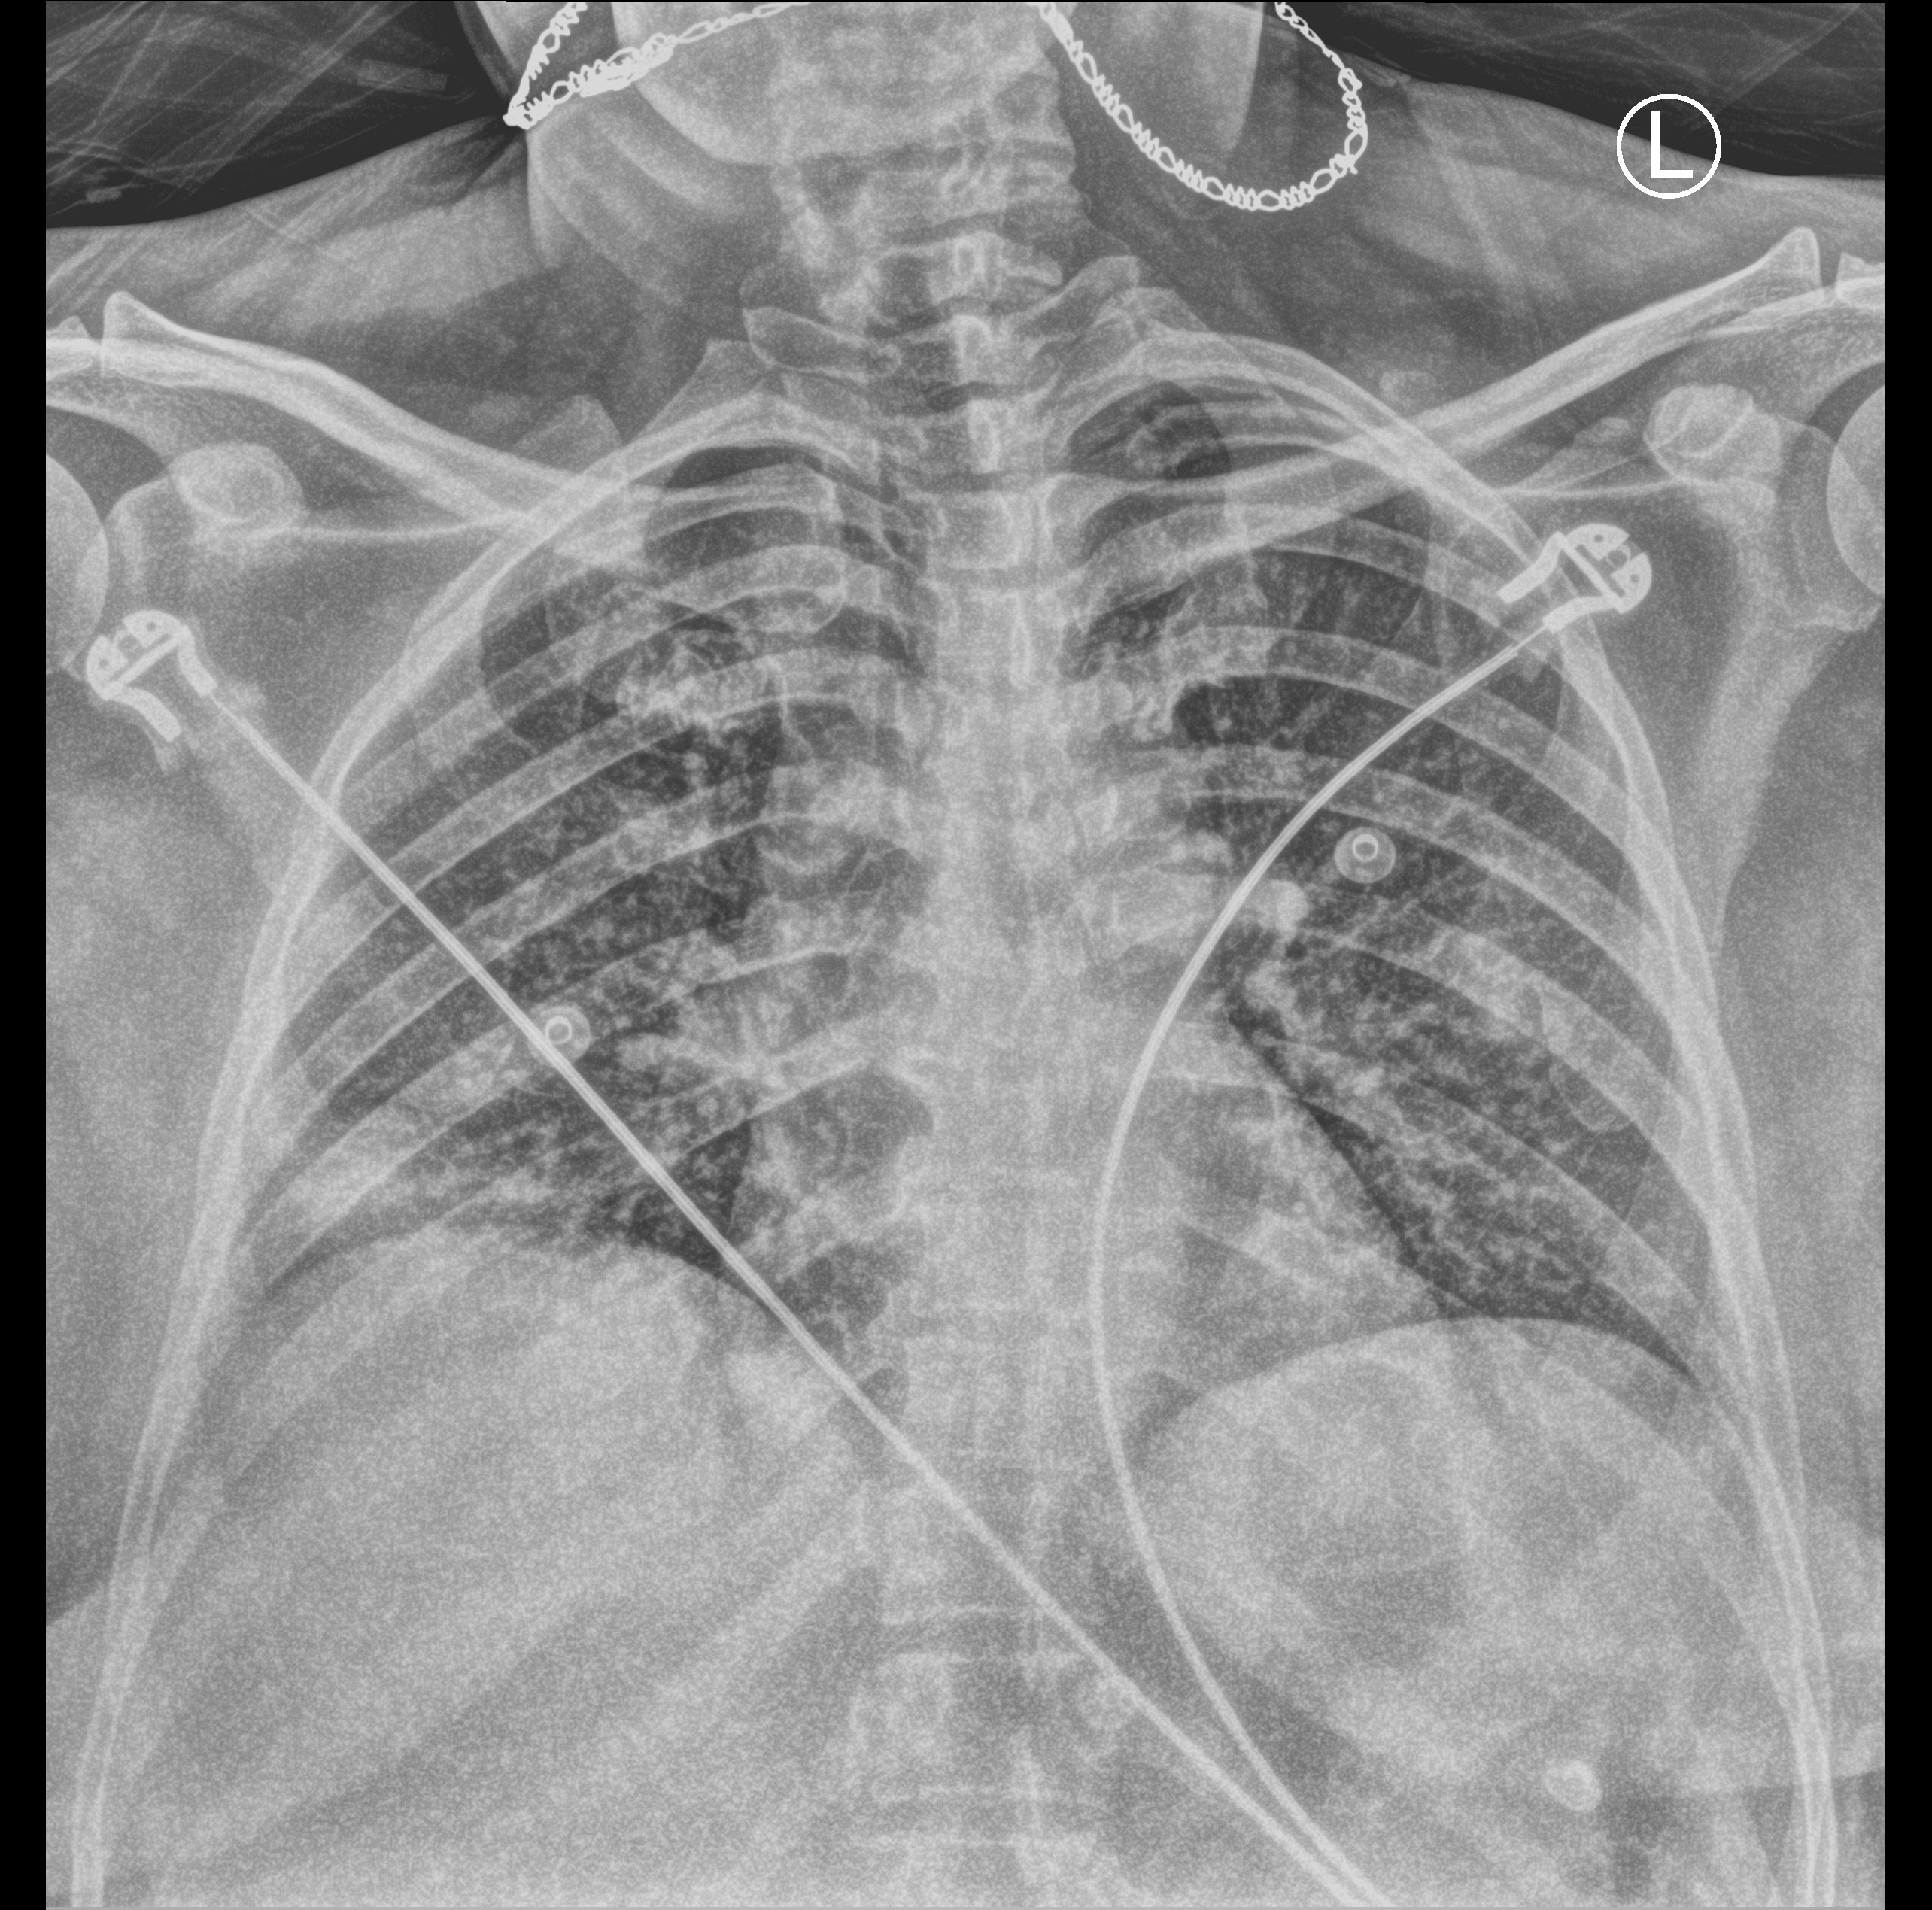
Chest X-ray (portable), anteroposterior (AP) projection. Female patient hospitalised with COVID-19, age 18–59 years.
Admission-level facts for this patient (not findings on this image; timing relative to this image not recorded): length of hospital stay: 5 days.